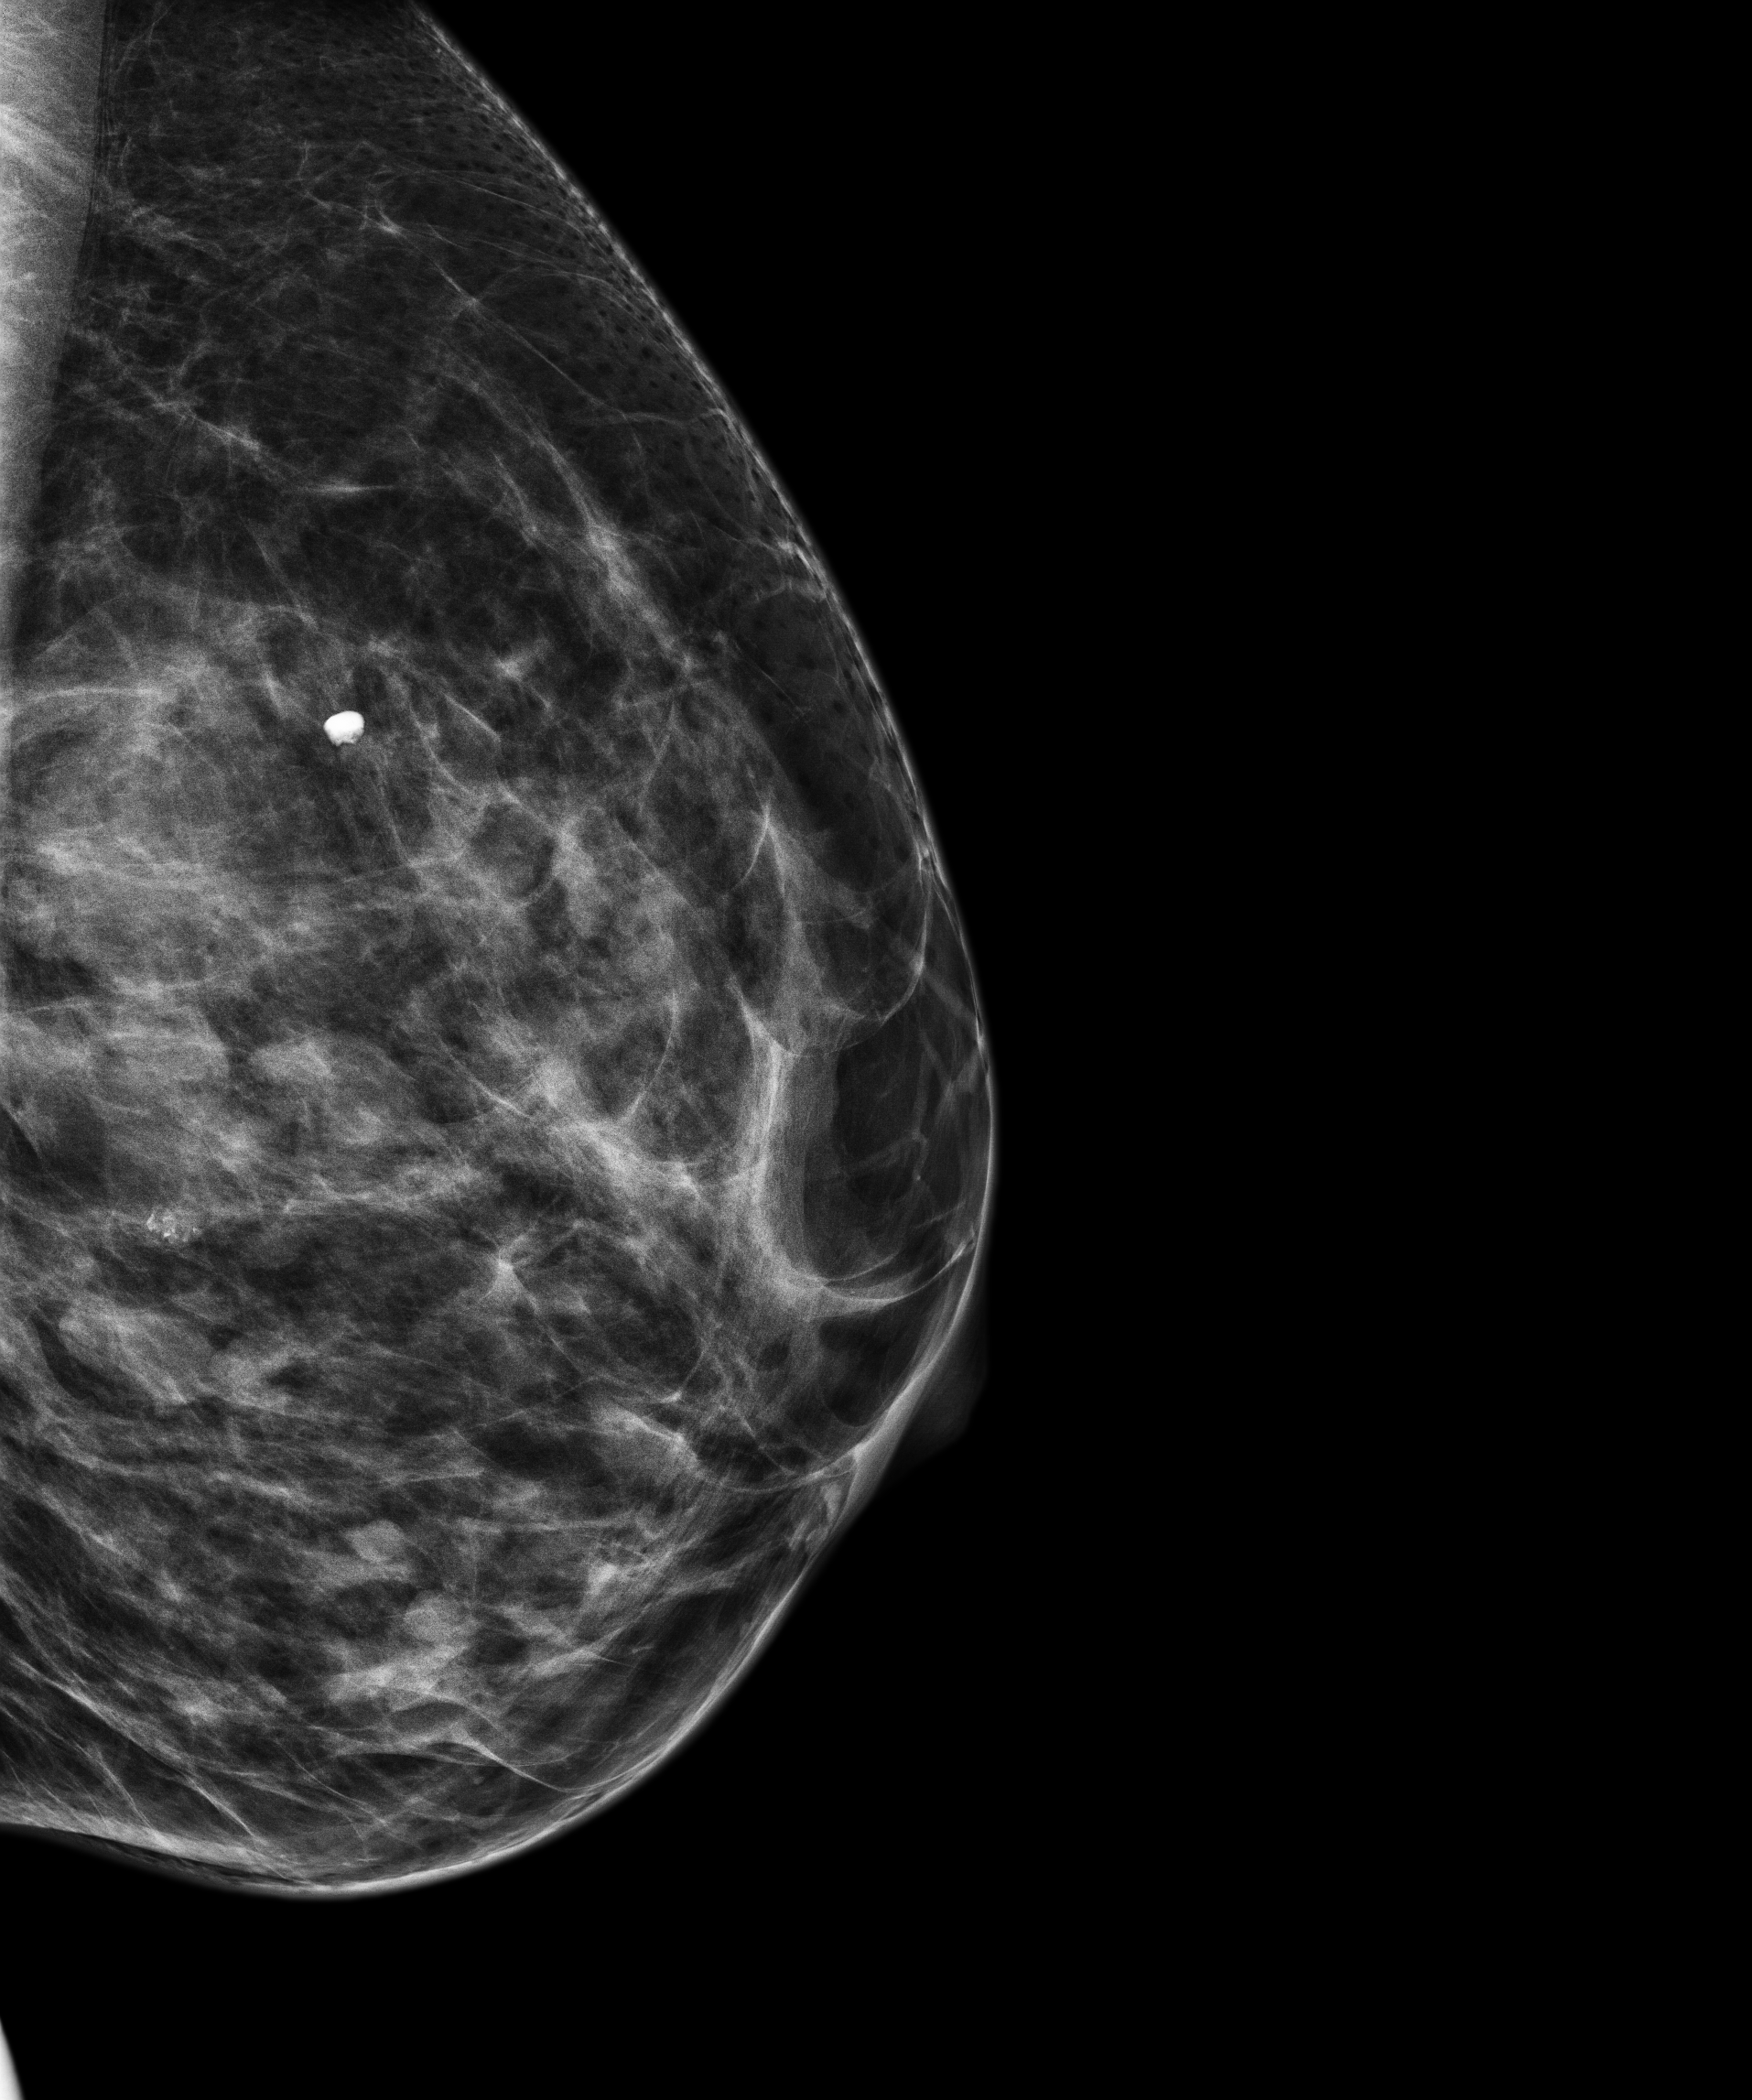
Diagnostic examination (additional views), system: Senographe Pristina. Female patient, age 52 years.
Image type: full-field digital mammogram. Breast: left. Projection: LM view.